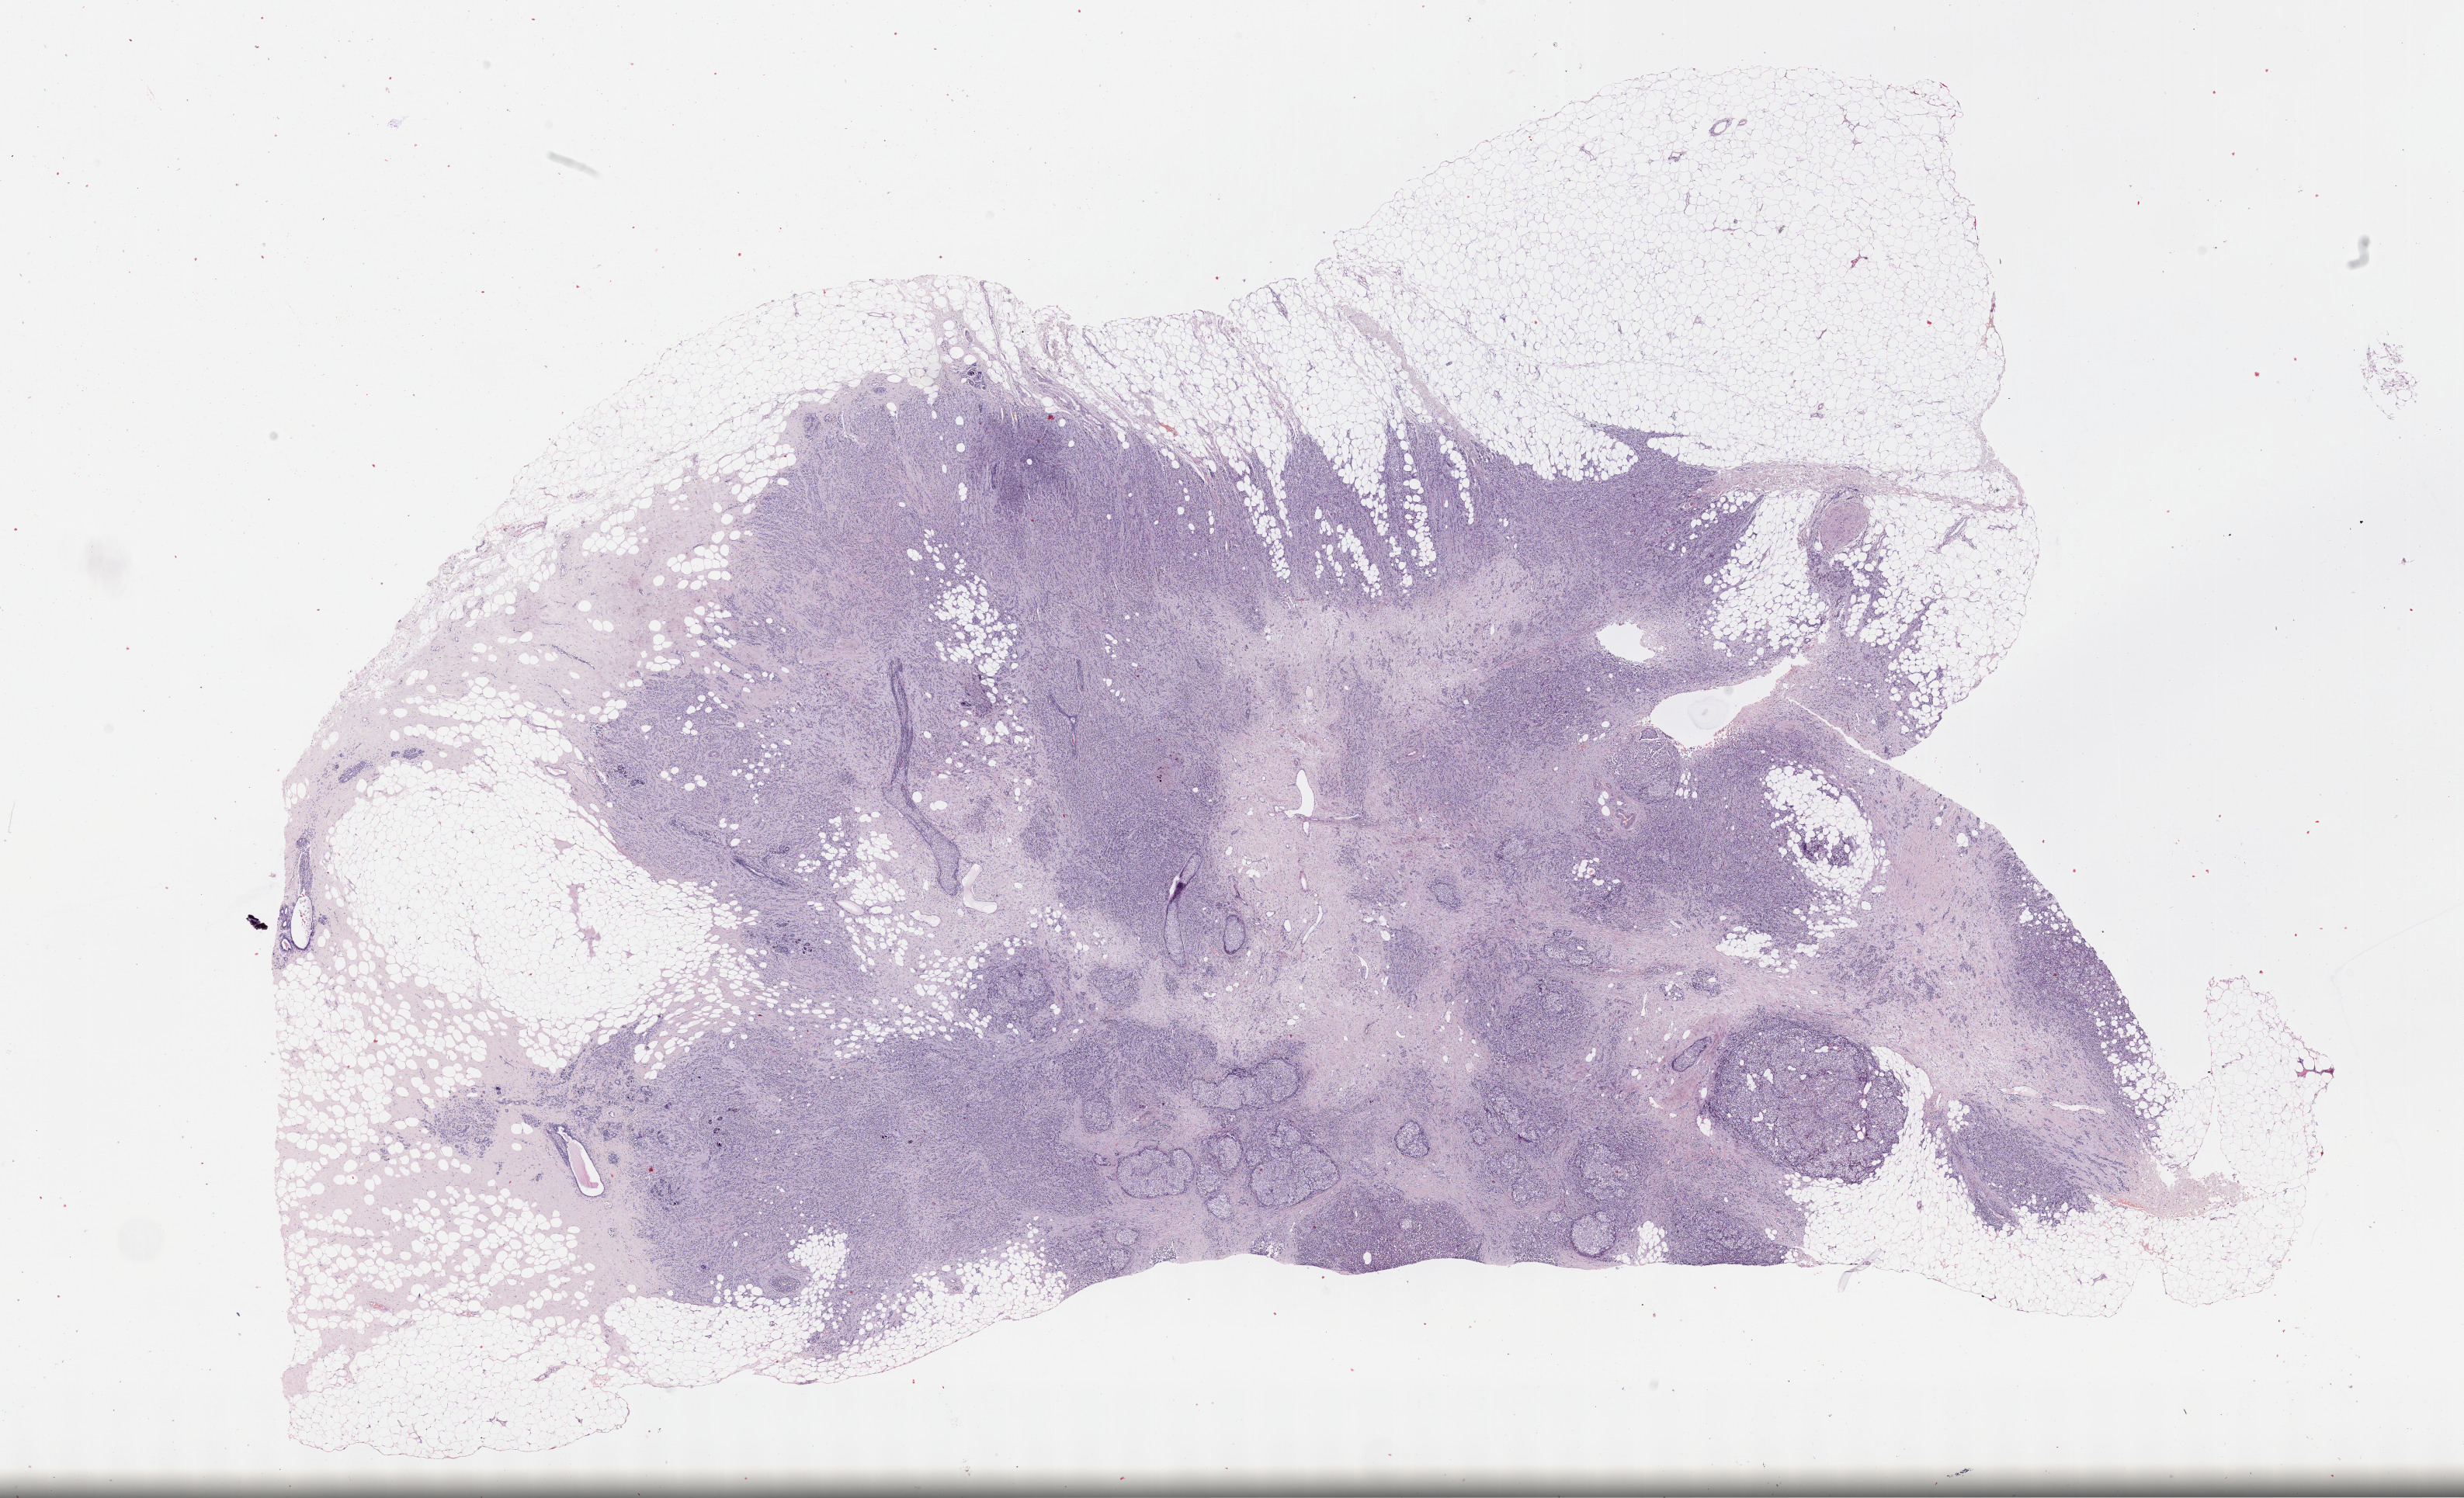
Whole-slide histology image, H&E-stained — shown as a low-resolution overview of the whole scanned area (about 25.7 x 15.6 mm, slide scanned at 40x). Formalin-fixed paraffin-embedded (FFPE) diagnostic section. Breast, primary tumour sample. Patient: female, age at initial diagnosis 54 years.
Lymph nodes positive (case pathology): 2 of 22 examined. Pathologic diagnosis: Infiltrating duct carcinoma, NOS. AJCC pathologic stage: IIA (7th edition).